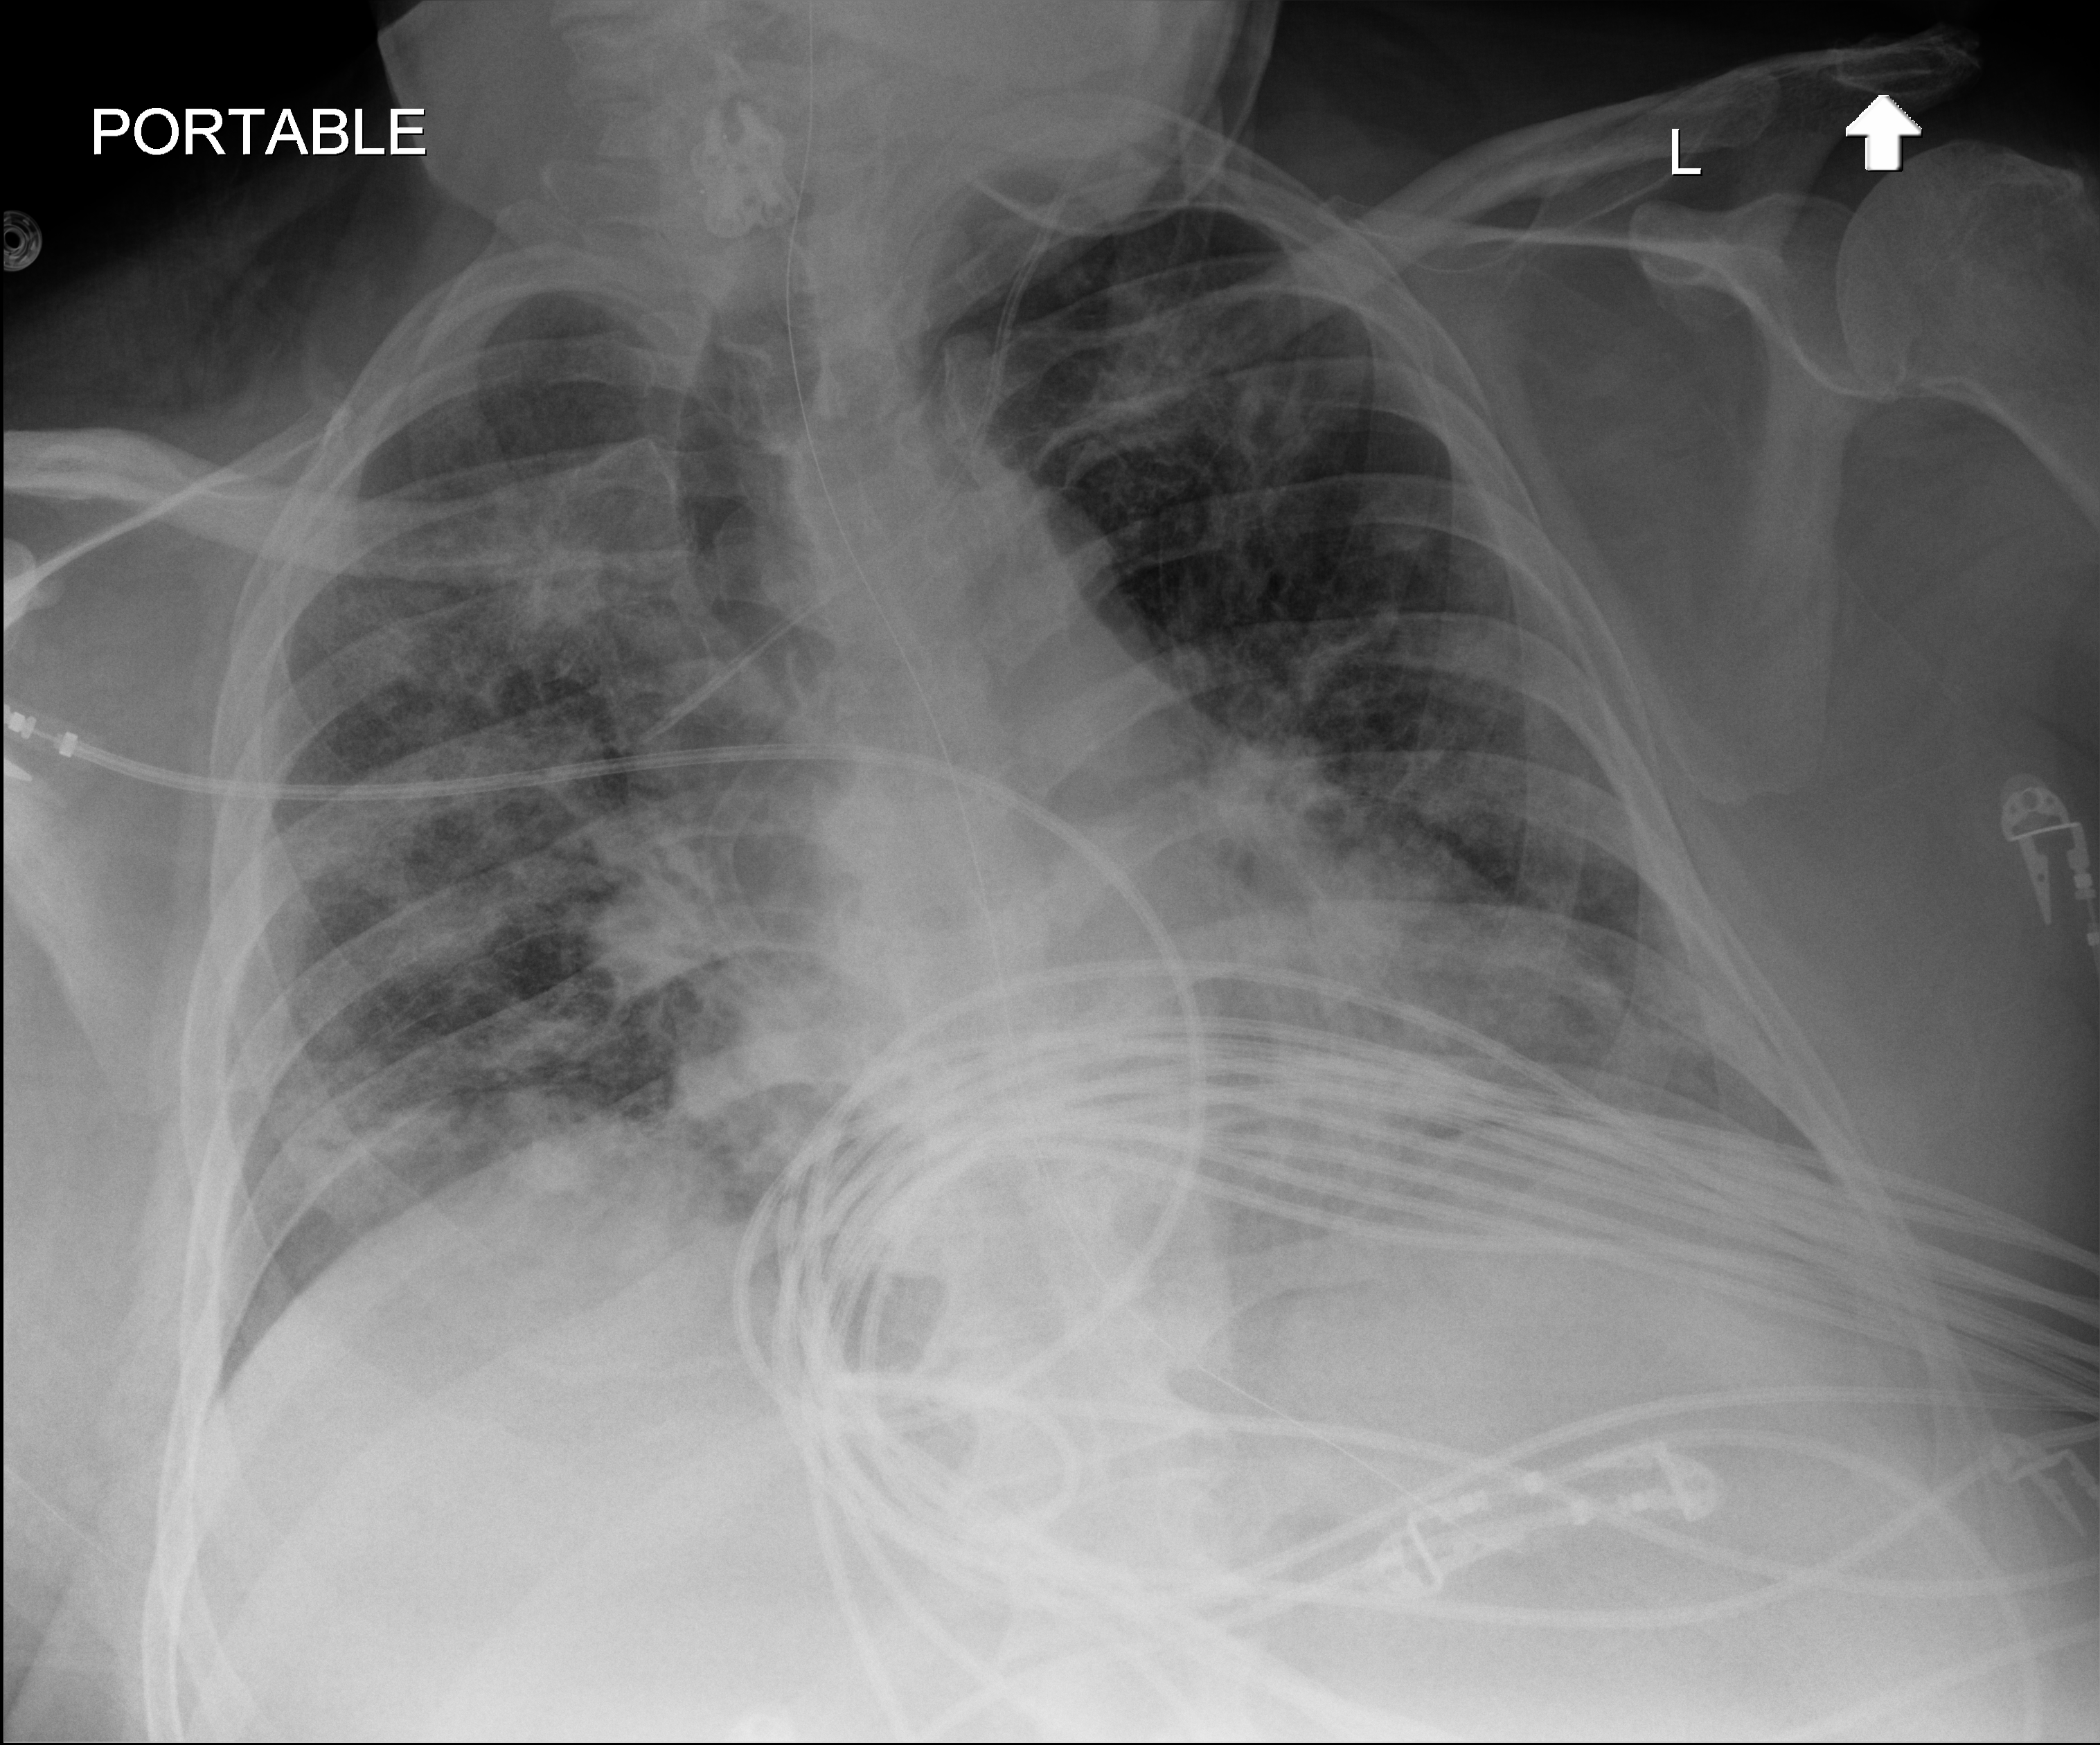
Chest radiograph (digital radiography), anteroposterior (AP) projection. Male patient hospitalised with COVID-19, age 18–59 years.
Admission-level facts for this patient (not findings on this image; timing relative to this image not recorded):
- diabetes (admission record): no